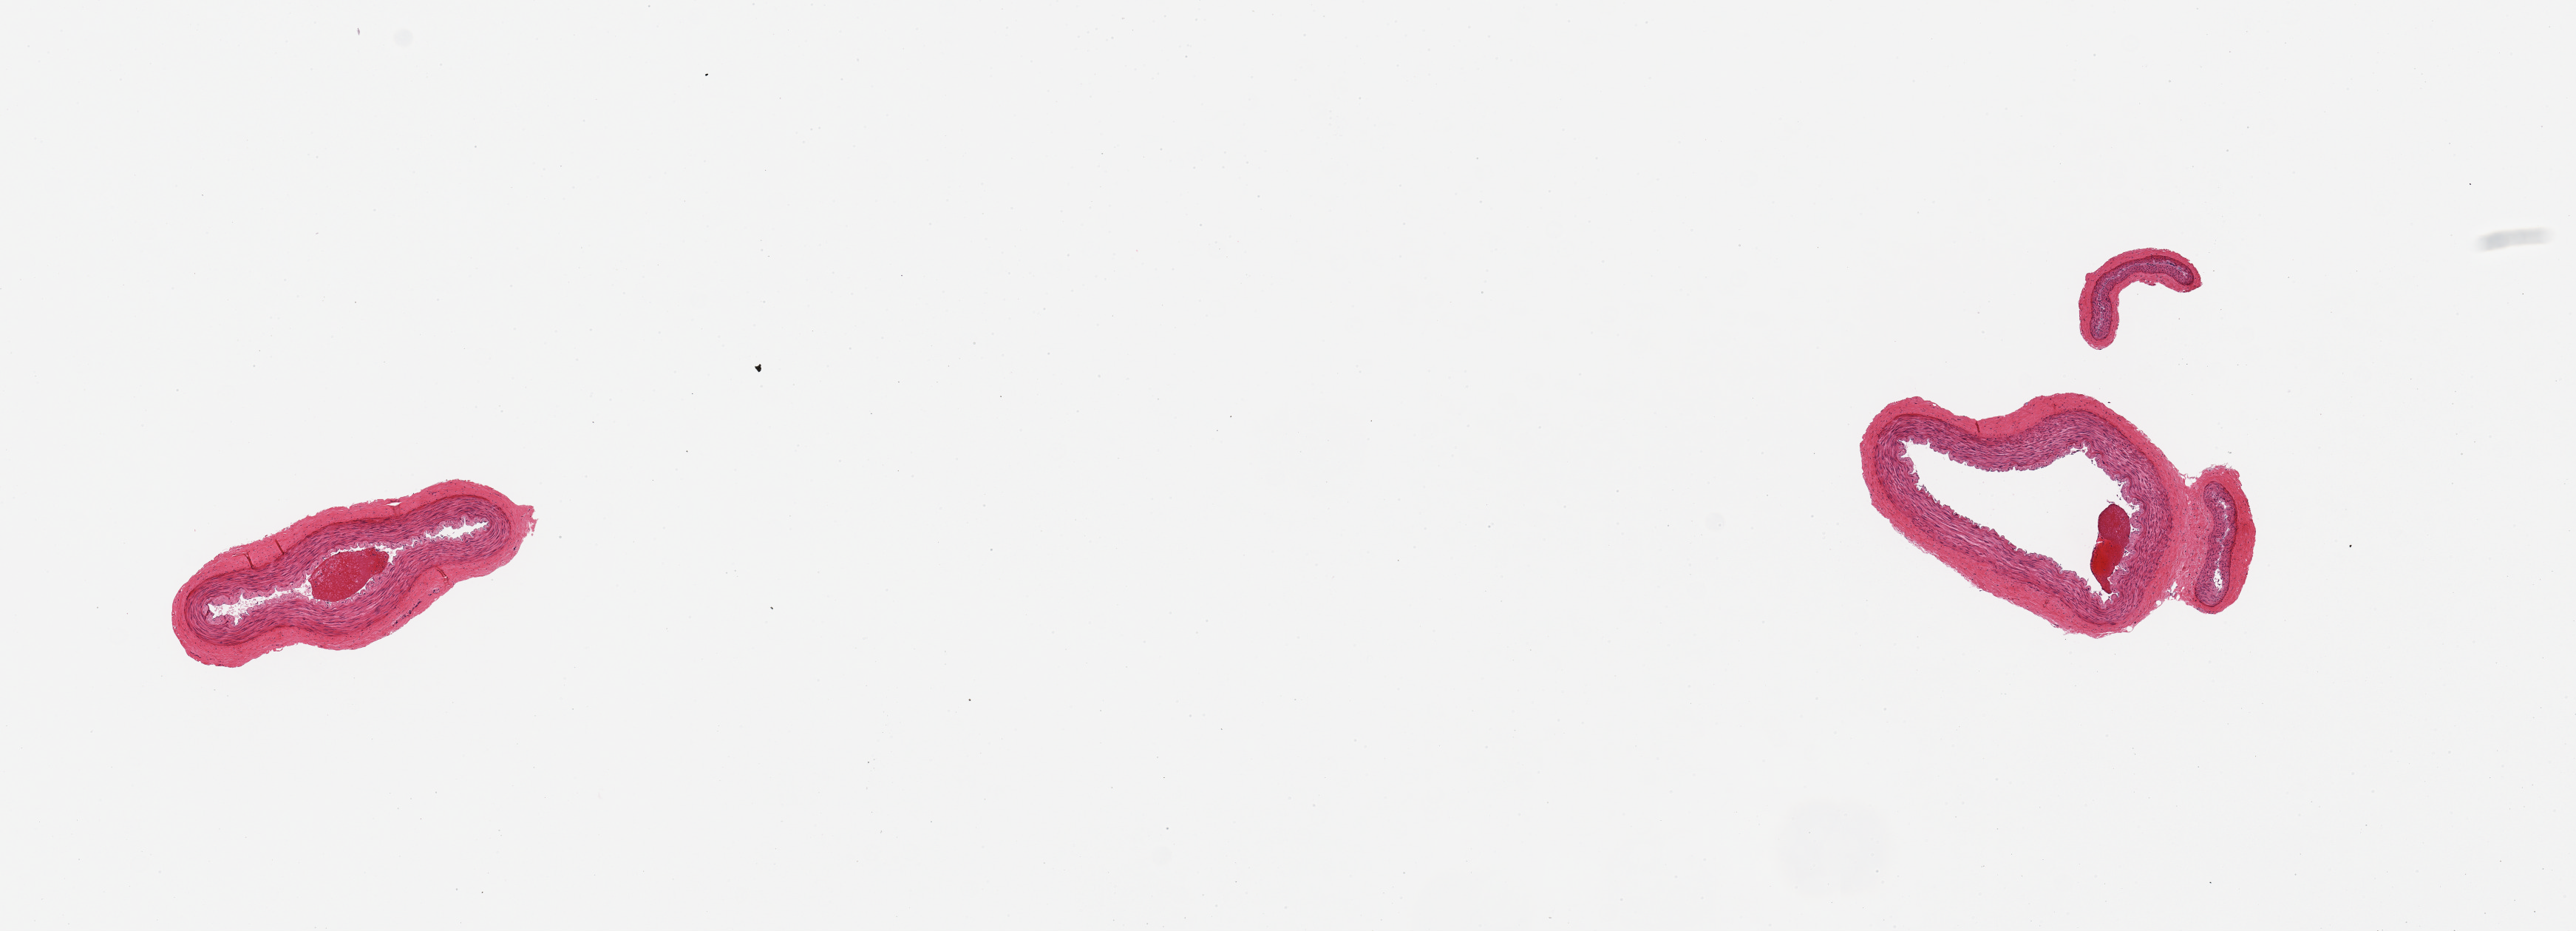
Whole-slide image, hematoxylin and eosin (H&E) stain — shown as a low-resolution overview of the whole scanned area (about 13.8 x 5.0 mm, slide scanned at 20x). PAXgene-fixed paraffin-embedded (PFPE) section. Sampled site (target tissue): tibial artery. Donor tissue sample. Female donor.
Review note (as recorded): 2 pieces, no adhrent fat or significant atherosis.